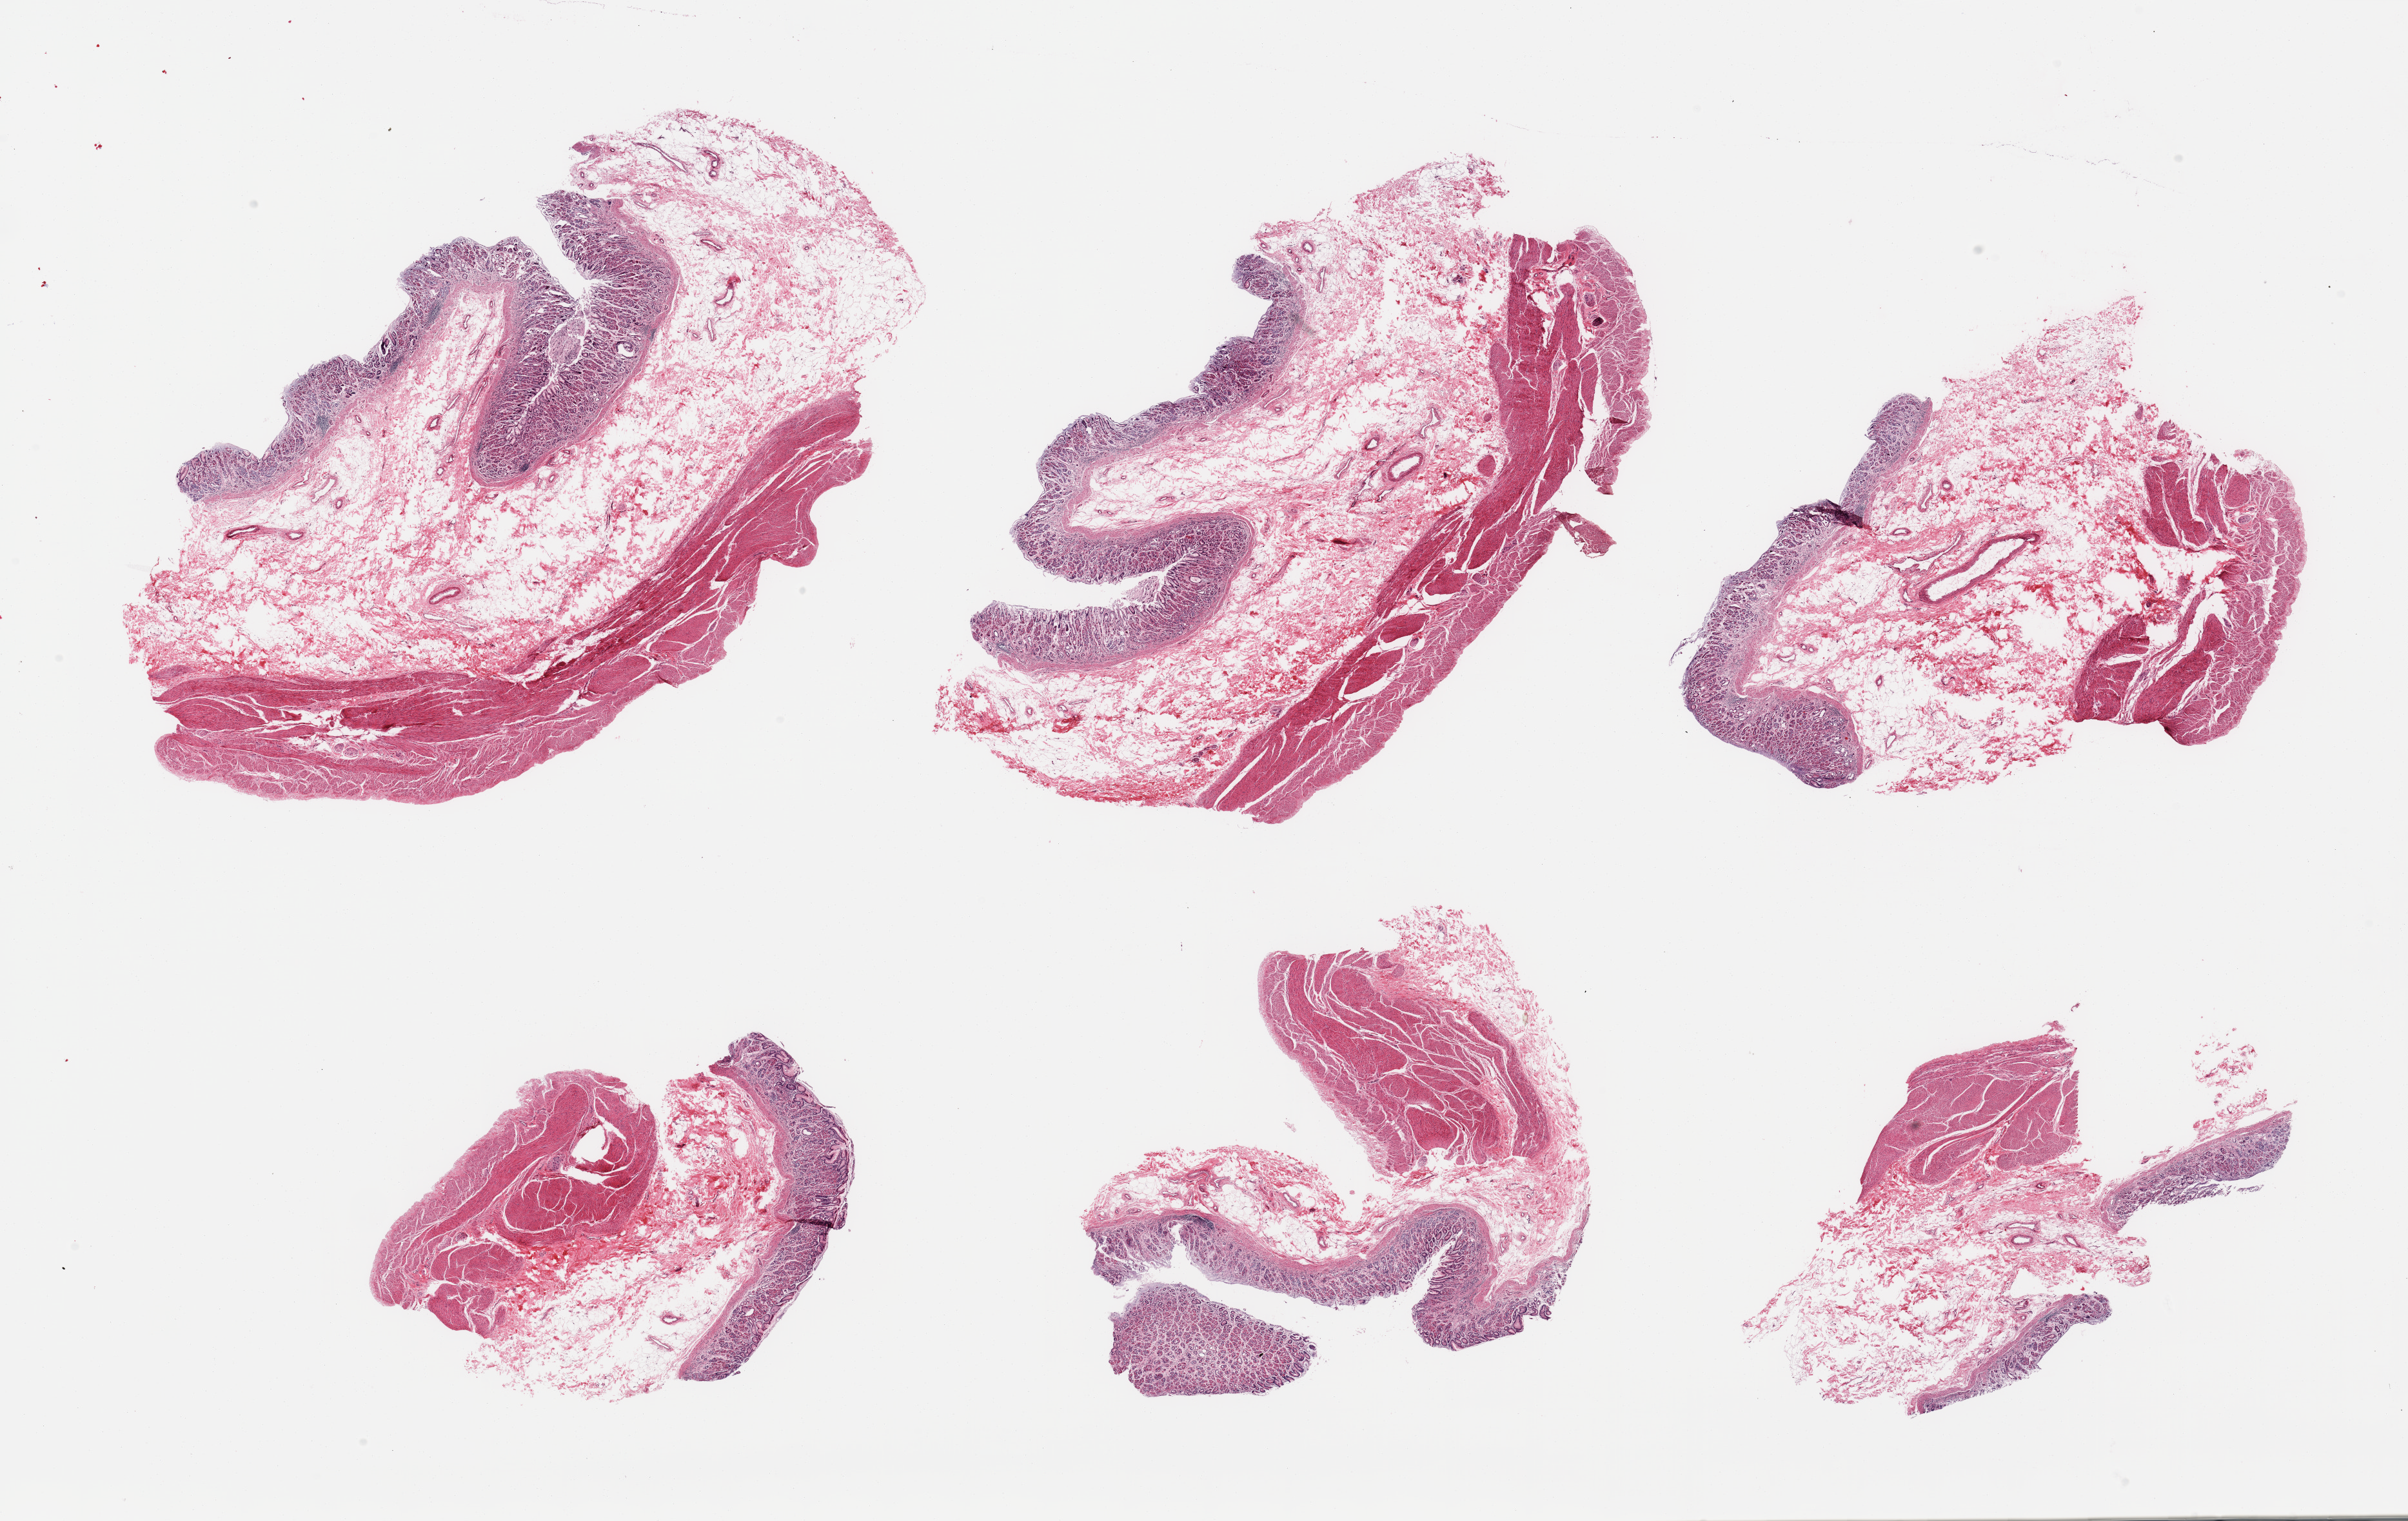
Digitized H&E-stained section — a low-resolution overview of the entire scanned area, about 29.5 x 18.7 mm (slide scanned at 20x); PAXgene-fixed, paraffin-embedded tissue; target tissue: stomach; tissue donor sample. Donor sex: male.
- pathologist's review note for this sample: 6 pieces, mucosa up to ~0.6mm, moderately advanced autolysis